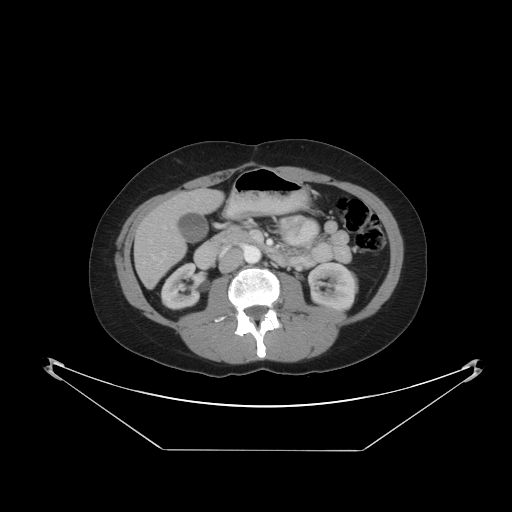
Contrast-enhanced abdominal CT, one axial slice. Slice 16 of 48 in the series (ordered by position). Reconstruction kernel STANDARD. 120 kVp. Intravenous contrast given. Soft-tissue window (W 400 / L 40 HU). 5 mm slice thickness. 512 × 512 image matrix. Female patient, age 38 years. From the clinical record (not read from this slice): diagnosis: colorectal cancer liver metastases, imaged before liver resection; multiple liver metastases: yes; largest metastasis: 2.5 cm.
Structures marked on this image (expert manual segmentation):
- hepatic veins: box from (x=164, y=227) to (x=166, y=229) px
- liver: (x=136, y=190)–(x=223, y=288)
- planned liver remnant (the part of the liver to remain after resection): (x=171, y=190)–(x=223, y=214)
- portal vein (with intrahepatic branches): (x=152, y=252)–(x=166, y=259)
- liver metastasis: (x=147, y=279)–(x=155, y=285)